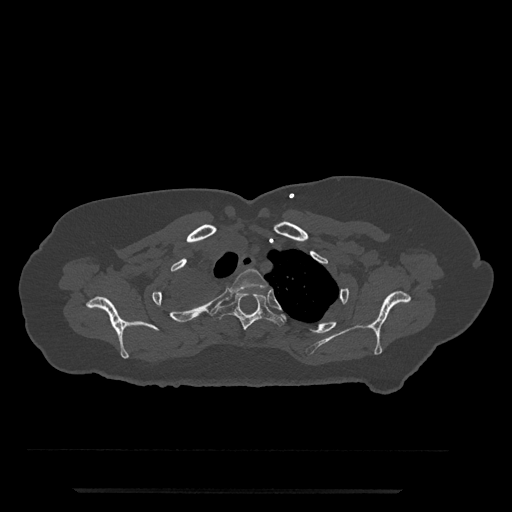
CT including the spine, one axial slice; position 643 of 797 along the scan axis; reconstruction kernel Br40s/3; 120 kVp; bone window (W 1800 / L 400 HU); 0.5 mm slice thickness; 512 × 512 image matrix, field of view 440 × 440 mm. Patient: female, 51 years. From the clinical record (not read from this slice): primary cancer: neuro; vertebrae with lytic lesions (as recorded): T8.
Annotated regions visible in this slice (semi-automatic segmentation, software-assisted and operator-edited):
- T2 vertebra: box from (x=230, y=269) to (x=267, y=294) px
- T3 vertebra: (x=213, y=291)–(x=286, y=330)